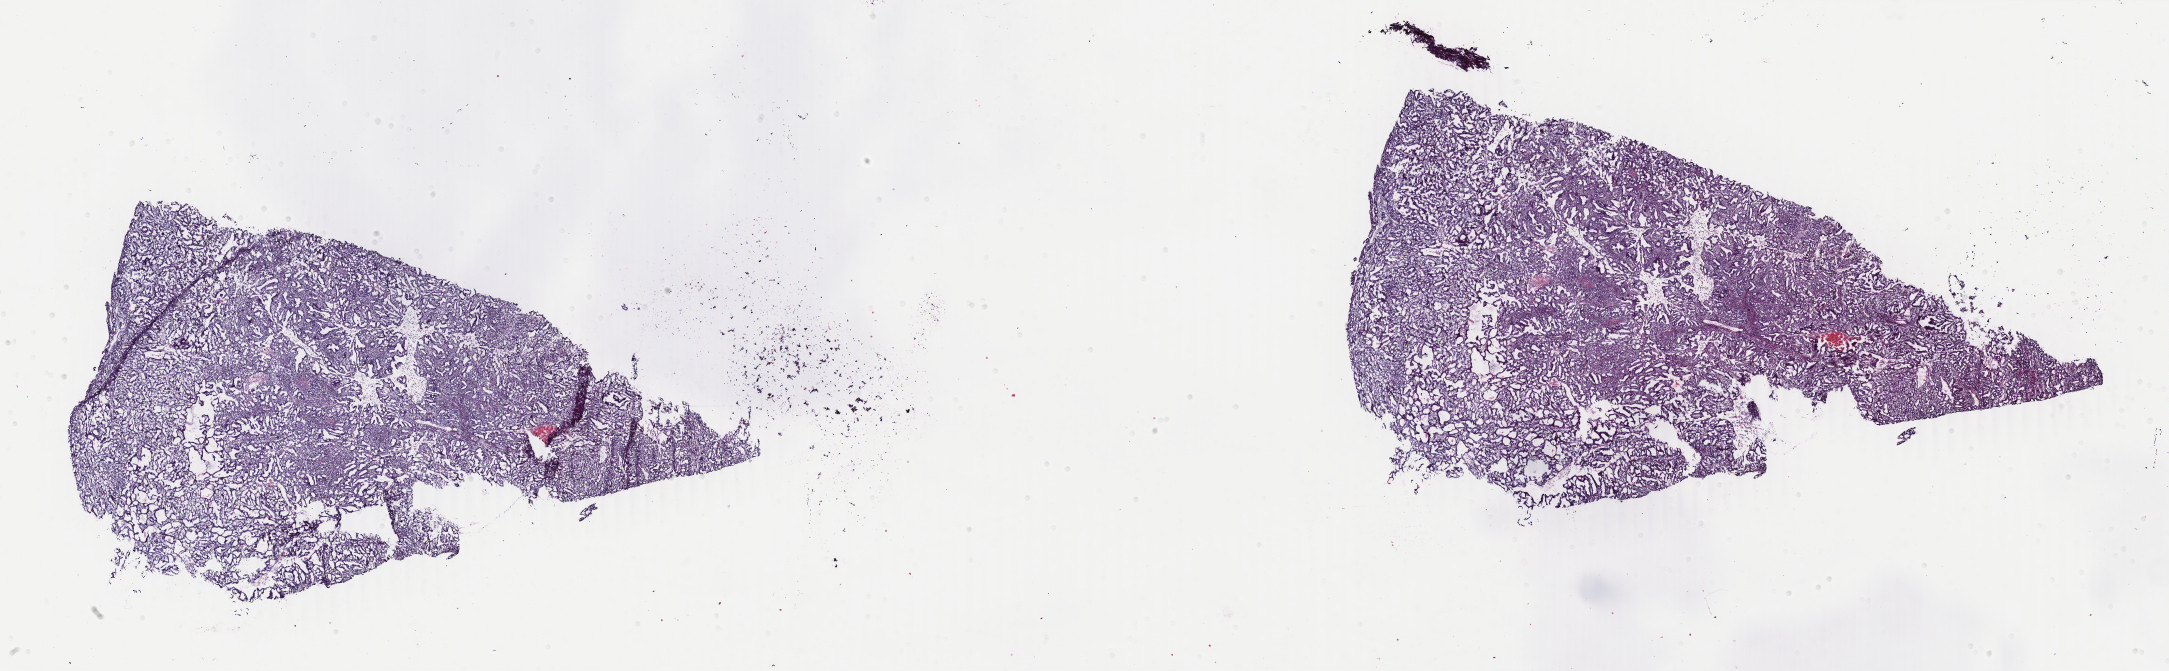
Whole-slide histology image, H&E-stained — shown as a low-resolution overview of the whole scanned area (about 34.5 x 10.7 mm, acquisition: 40x scan). Frozen section from the bottom of the tissue portion. Primary tumour sample from the uterus. Female, age 60 years at initial diagnosis. Histologic grade: G3 (poorly differentiated). Composition of this section per pathologist review: tumour cells 60%, tumour nuclei 70%, normal cells 0%, stromal cells 30%, necrosis 10%. Inflammatory infiltration, as recorded: lymphocyte infiltration 20%, monocyte infiltration 0%, neutrophil infiltration 10%.
FIGO stage: IIIC1. Diagnosis: Endometrioid adenocarcinoma, NOS.